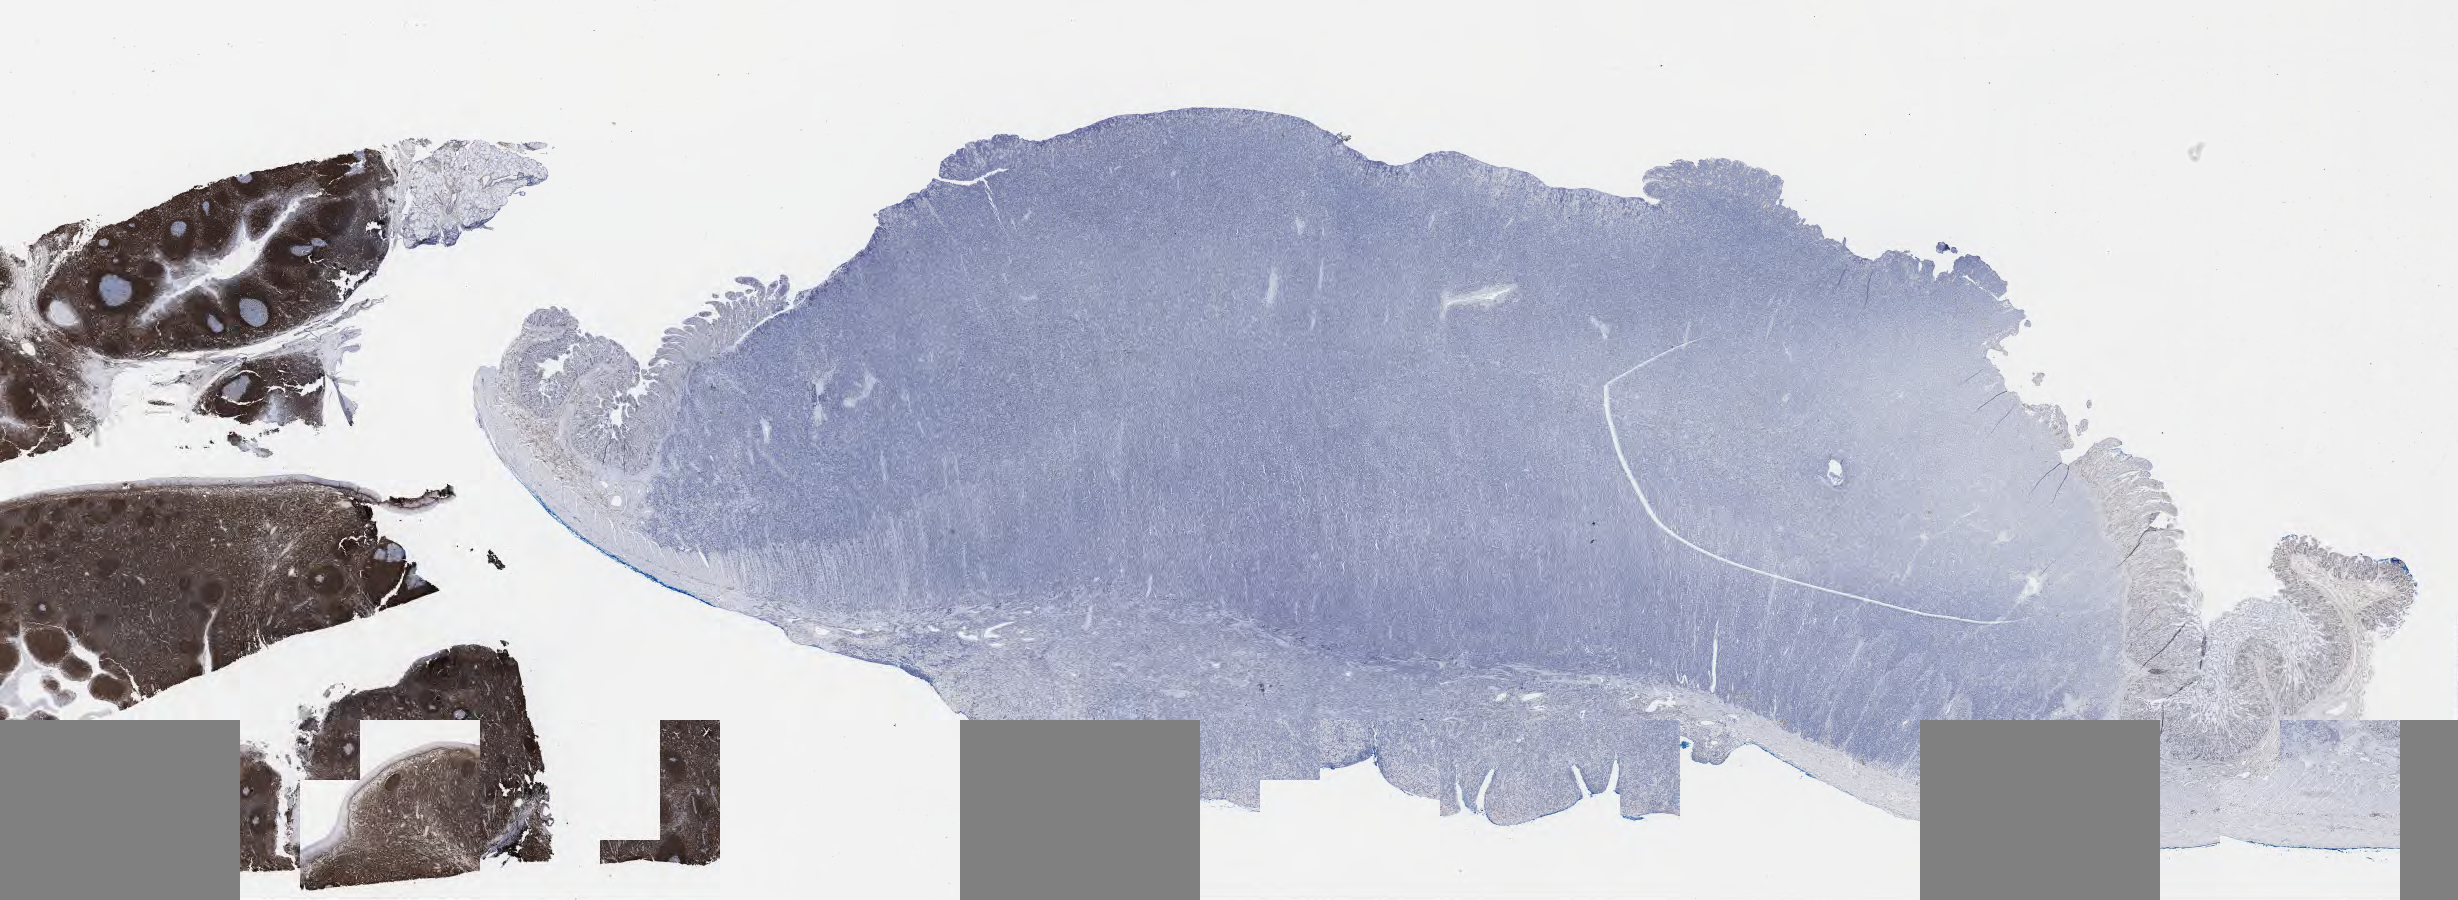
Immunohistochemistry (IHC) whole-slide image stained for BCL2 — low-resolution overview of the scanned area, about 39.7 x 14.5 mm; specimen: tumor tissue; site: small intestine. Male, age 6 years at initial diagnosis.
Diagnosis: Burkitt lymphoma, NOS.